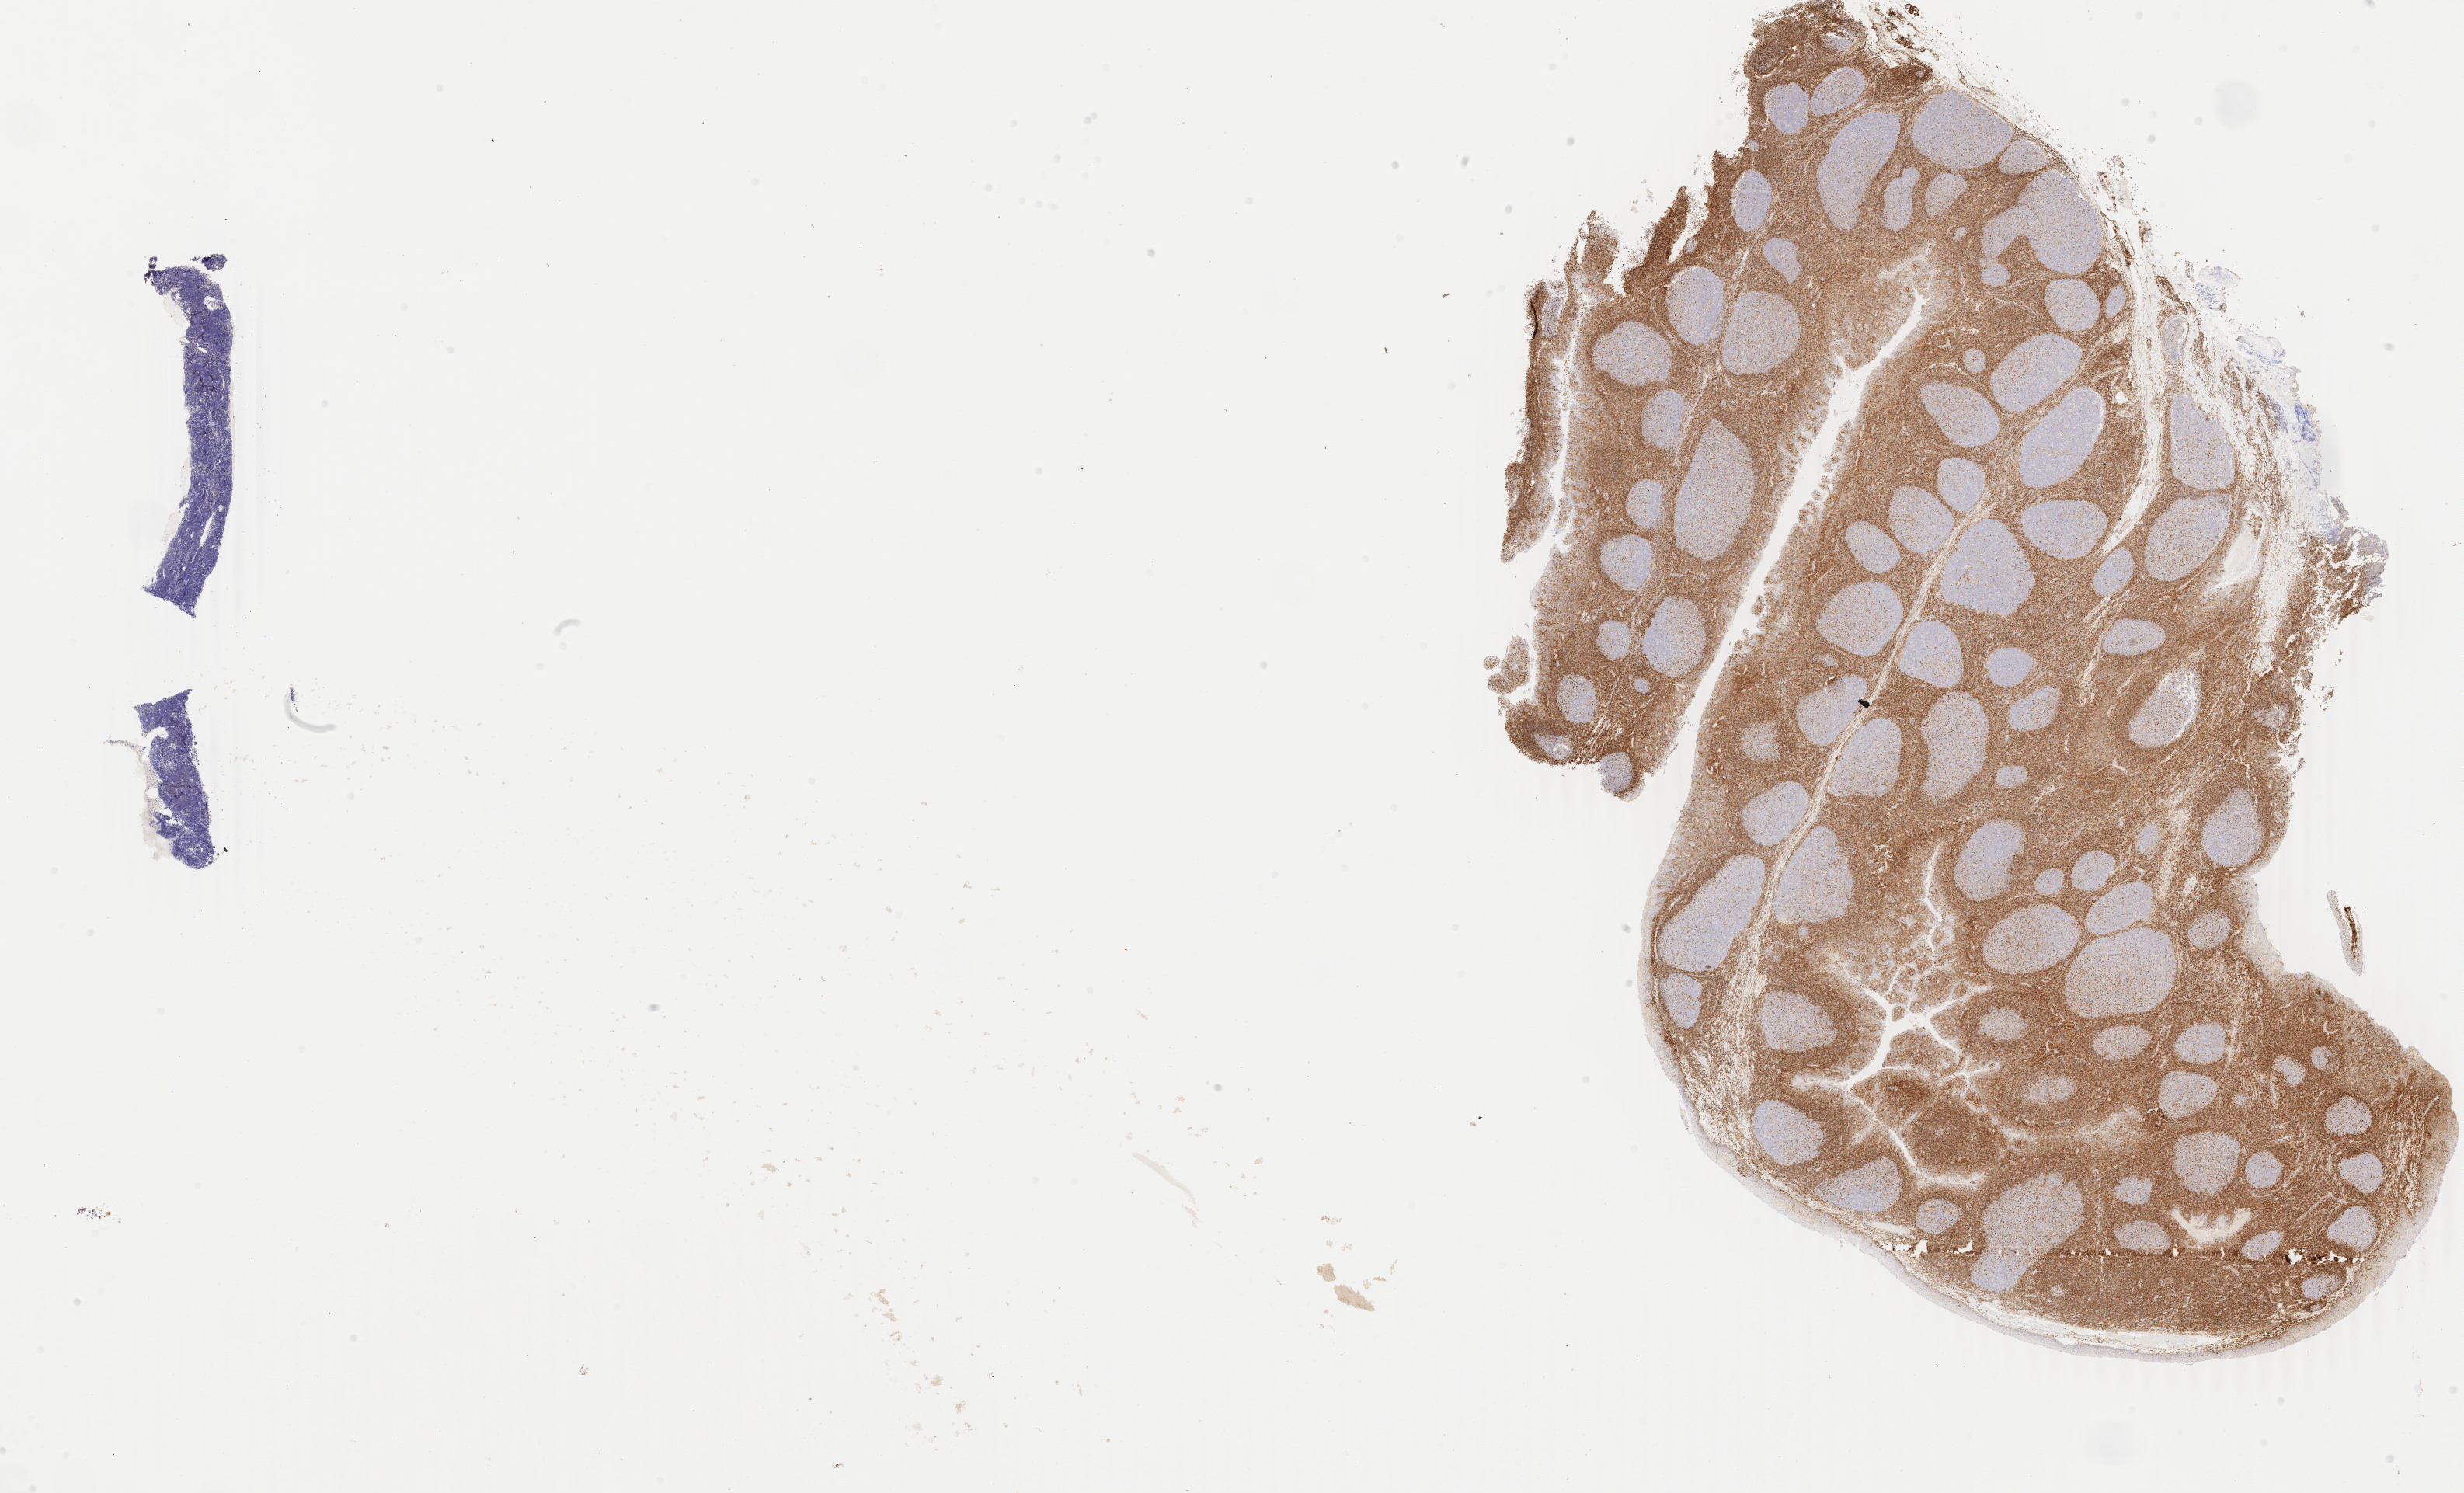
Immunohistochemistry (IHC) whole-slide image stained for BCL2 — low-resolution overview of the scanned area, about 25.2 x 15.3 mm; tumor tissue; anatomic site: abdominal lymph node. Female, age 6 years at initial diagnosis.
Diagnosis: Burkitt lymphoma, NOS.